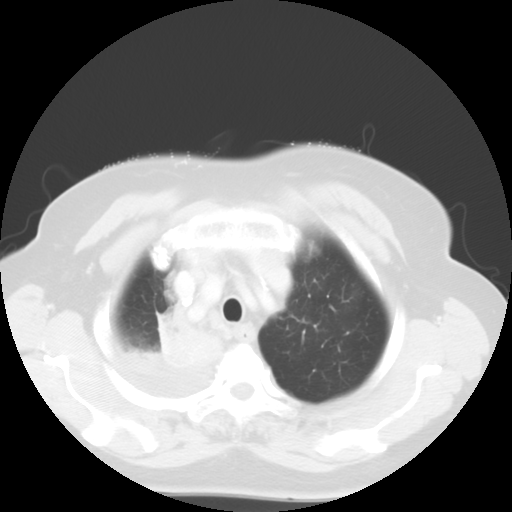
Chest CT, one axial slice; position 45 of 52 along the scan axis; reconstruction kernel STANDARD; 120 kVp; lung window (W 1500 / L -600 HU); 5 mm slice thickness; 512 × 512 image matrix, field of view 333 × 333 mm. Female patient, age 81 years. From the clinical record (not read from this slice): clinical TNM (as recorded): T4 N3 M1b.
Outlined on this slice (rectangle marked by the reading radiologist):
- lung tumour (recorded histology: adenocarcinoma): bounding box (x1, y1, x2, y2) in pixels: (154, 310, 223, 375)